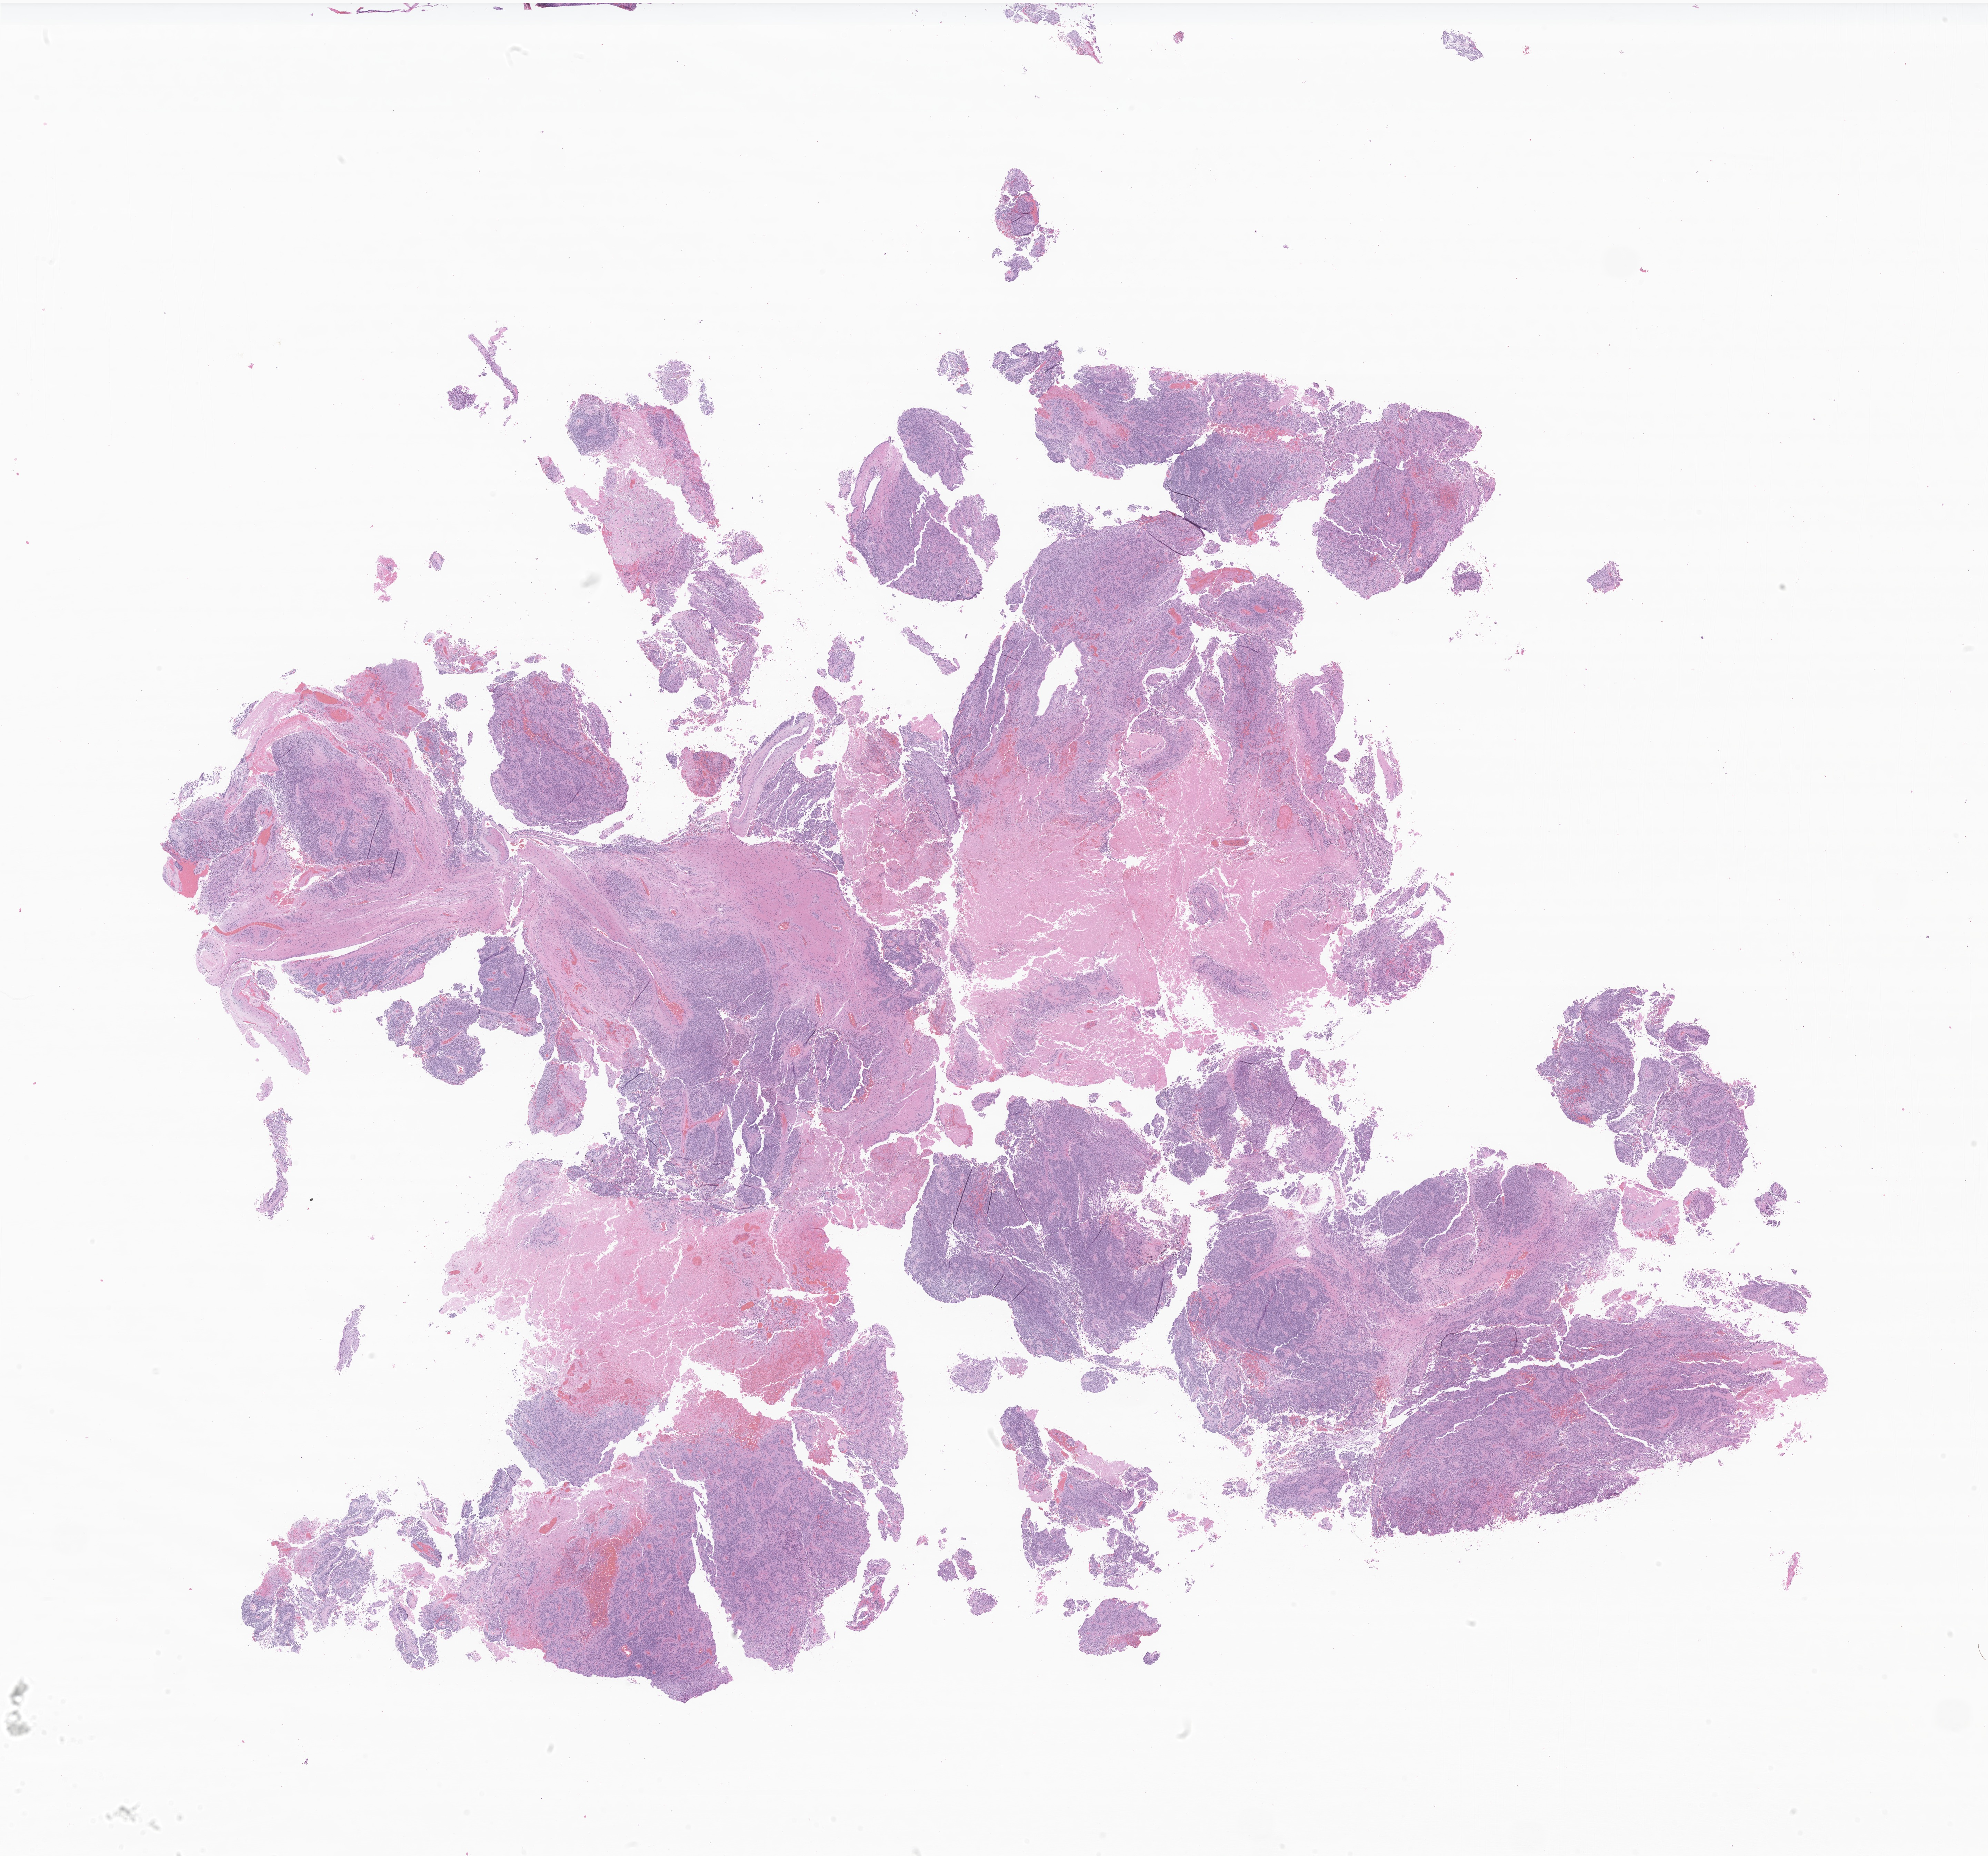
Haematoxylin and eosin whole-slide image of tumor tissue from the brain, a low-resolution overview of the entire scanned area, about 24.3 x 22.7 mm. Formalin-fixed, paraffin-embedded (FFPE) tissue. Male patient, age 85 months.
Diagnosis (ICD-O-3 morphology term): Ependymoma, NOS.